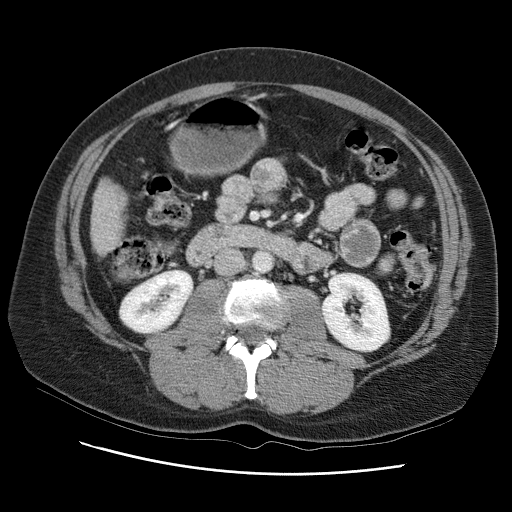
Contrast-enhanced abdominal CT (liver protocol), one axial slice. Slice 22 of 95 in the series (ordered by position). Reconstruction kernel STANDARD. One of 2 acquisitions stored at this slice position. Soft-tissue window (W 400 / L 40 HU). 512 × 512 image matrix. From the clinical record (not read from this slice): diagnosis: hepatocellular carcinoma (patient treated with transarterial chemoembolisation; whether this scan precedes or follows treatment is not stated here); TNM stage (as recorded): Stage-I; Child-Pugh class: B; tumour differentiation: moderately differentiated; tumour nodularity: uninodular.
Outlined on this slice (semi-automatic segmentation, software-assisted and operator-edited):
- liver parenchyma outside the tumour (the mass and vessels are separate outlines, so this box may not span the whole liver): bounding box <92,162,140,260> (left, top, right, bottom; pixels)
- liver vessels: <104,181,120,229>